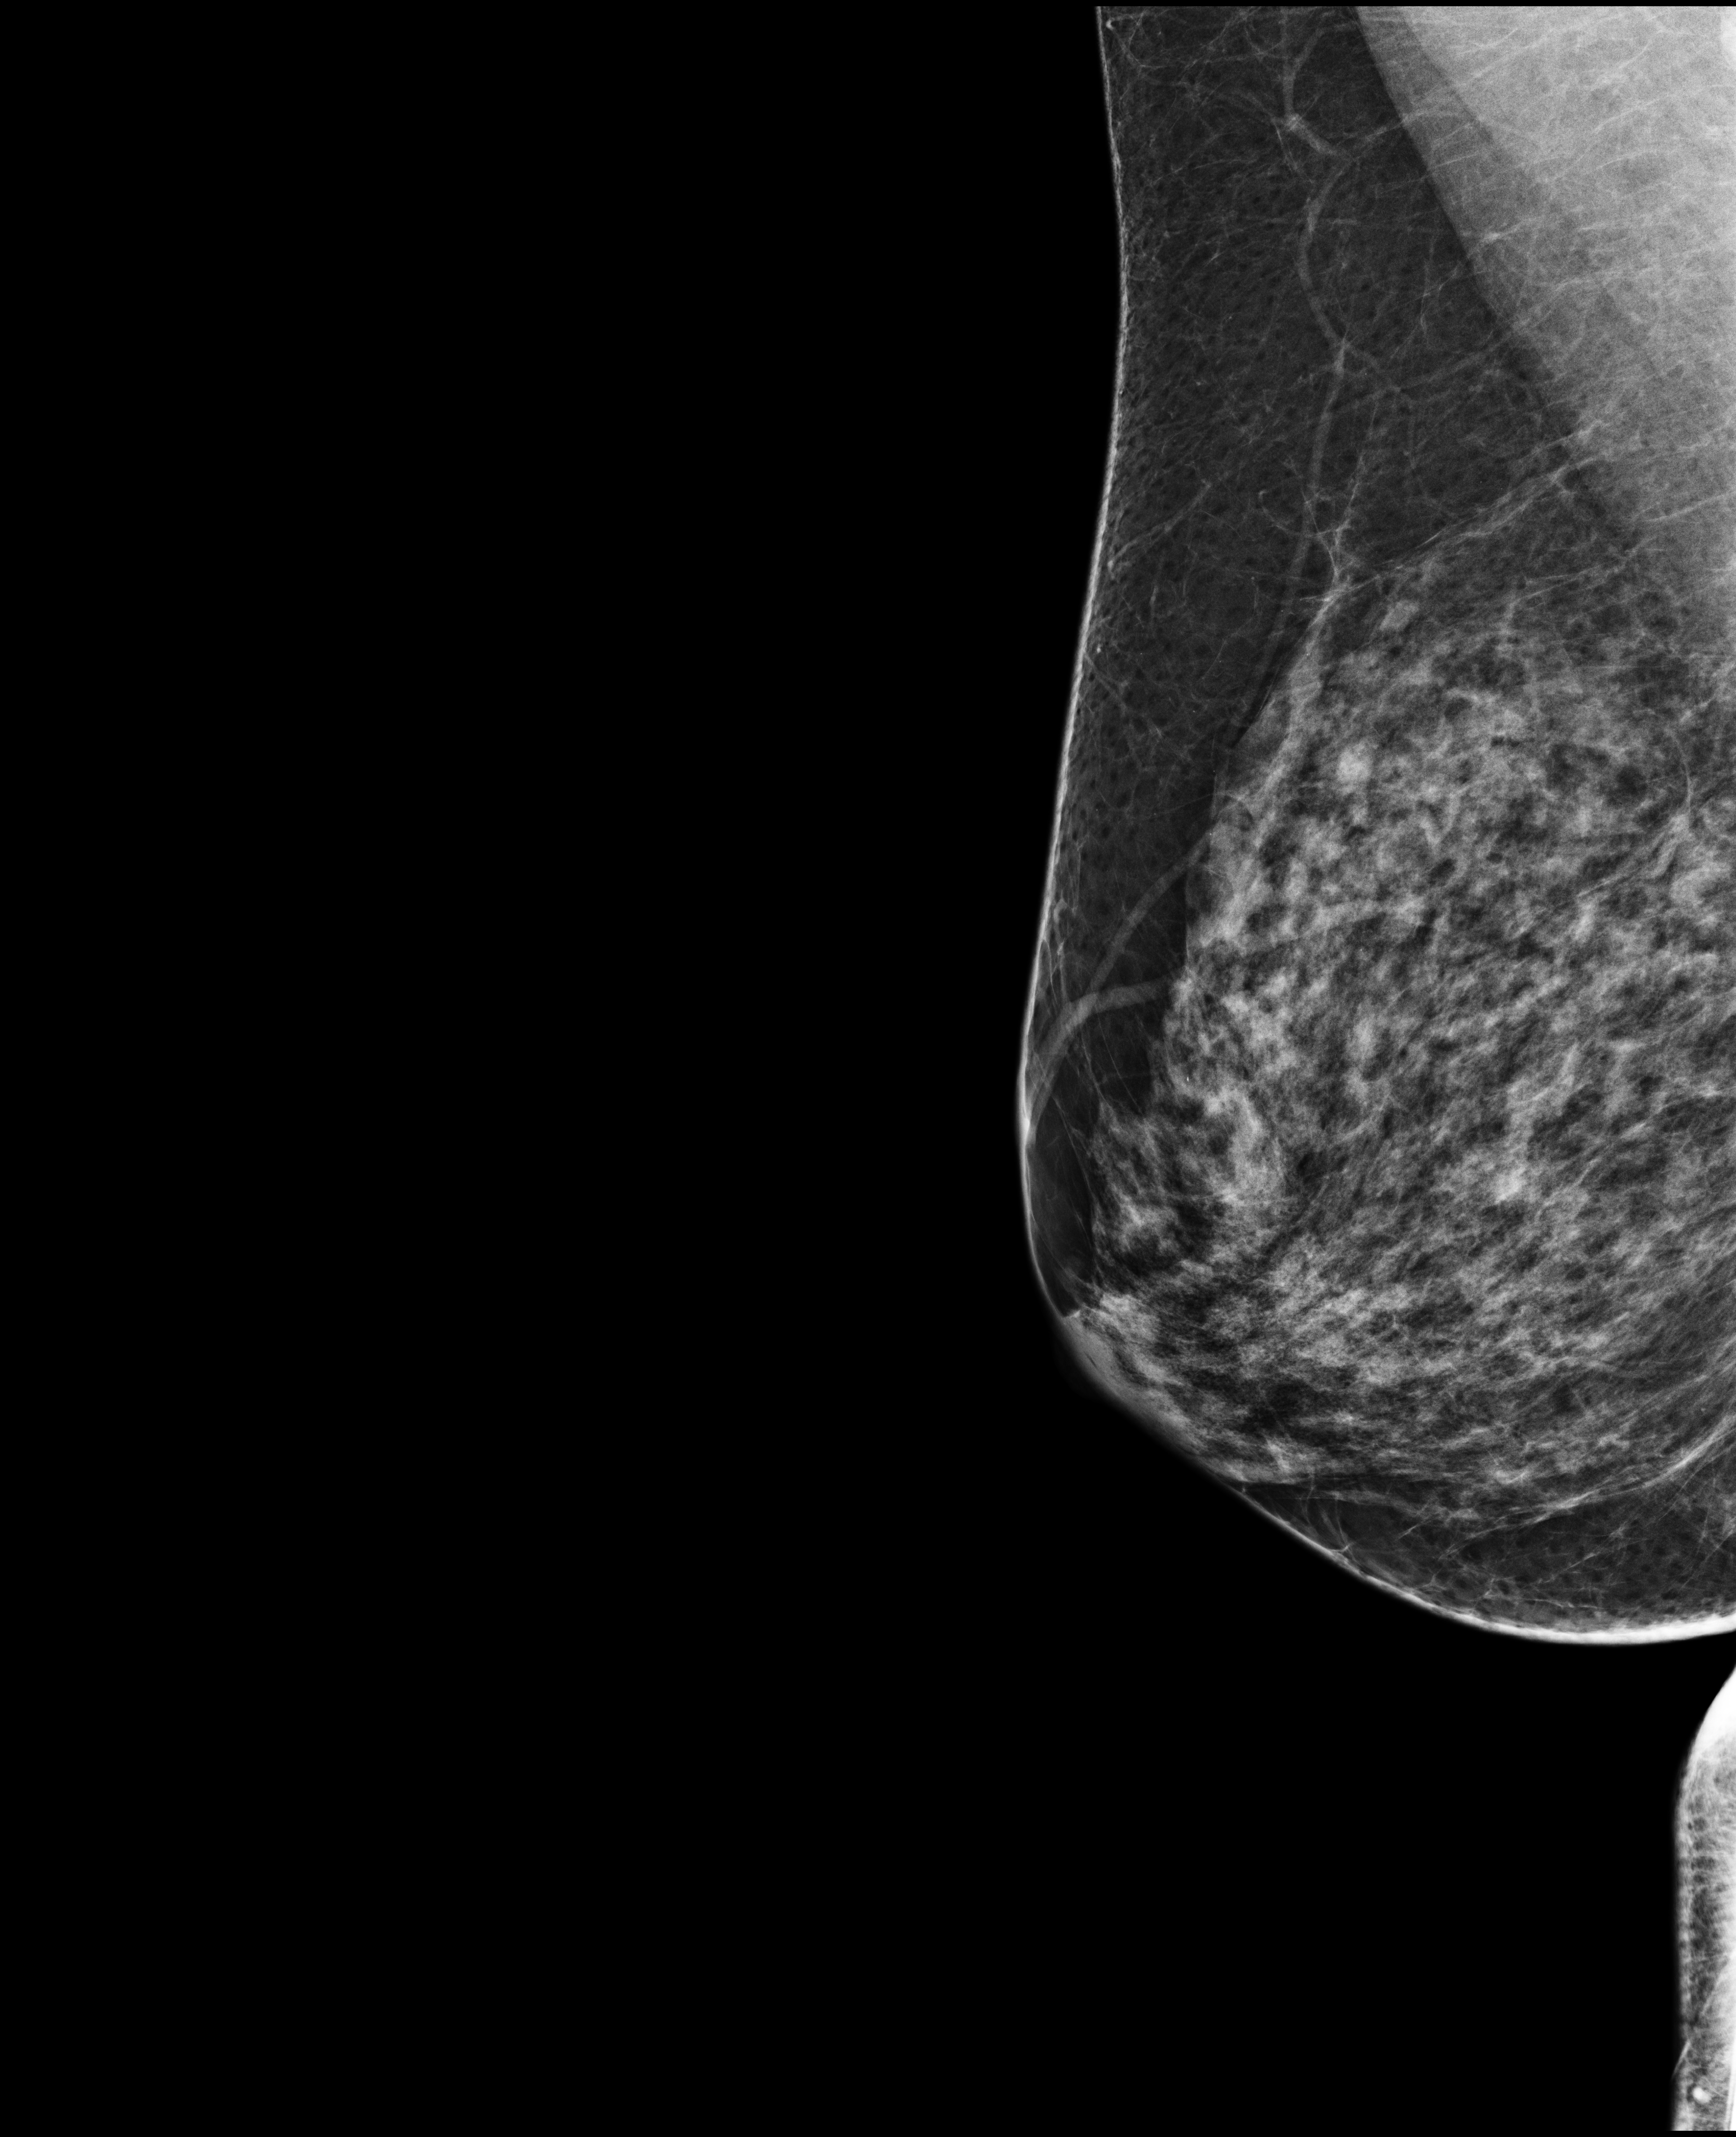
Screening examination, compressed breast thickness 71 mm. Patient aged 53 years (female).
Image type: full-field digital mammogram. Breast: right. Projection: MLO view.